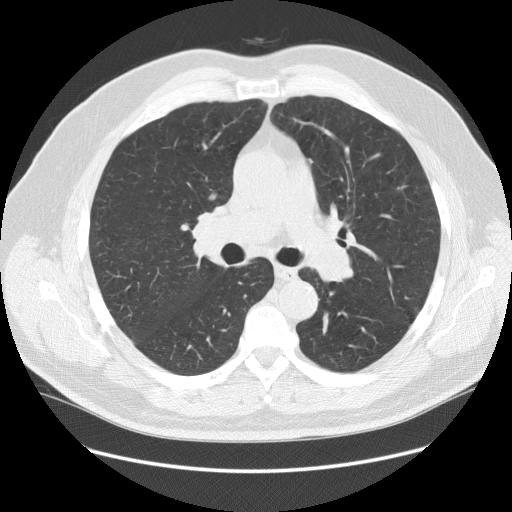
Low-dose screening chest CT, axial slice. First (baseline) screen. Lung window (W 1500 / L -600 HU). Slice 56 of 140 in the series. Male participant, aged 64 years at enrolment. Former smoker at enrolment.
Lesion marked by an expert reader, bounding box <180,196,247,268> (left, top, right, bottom; pixels). Screening reader's record for this exam (one nodule recorded; not confirmed to be the boxed lesion): non-calcified nodule or mass ≥4 mm, right lower lobe, 7 × 5 mm, smooth margins, soft tissue attenuation. Official screen result: positive, change unspecified: nodule(s) >= 4 mm or enlarging nodule(s), mass(es), or other non-specific abnormalities suspicious for lung cancer.